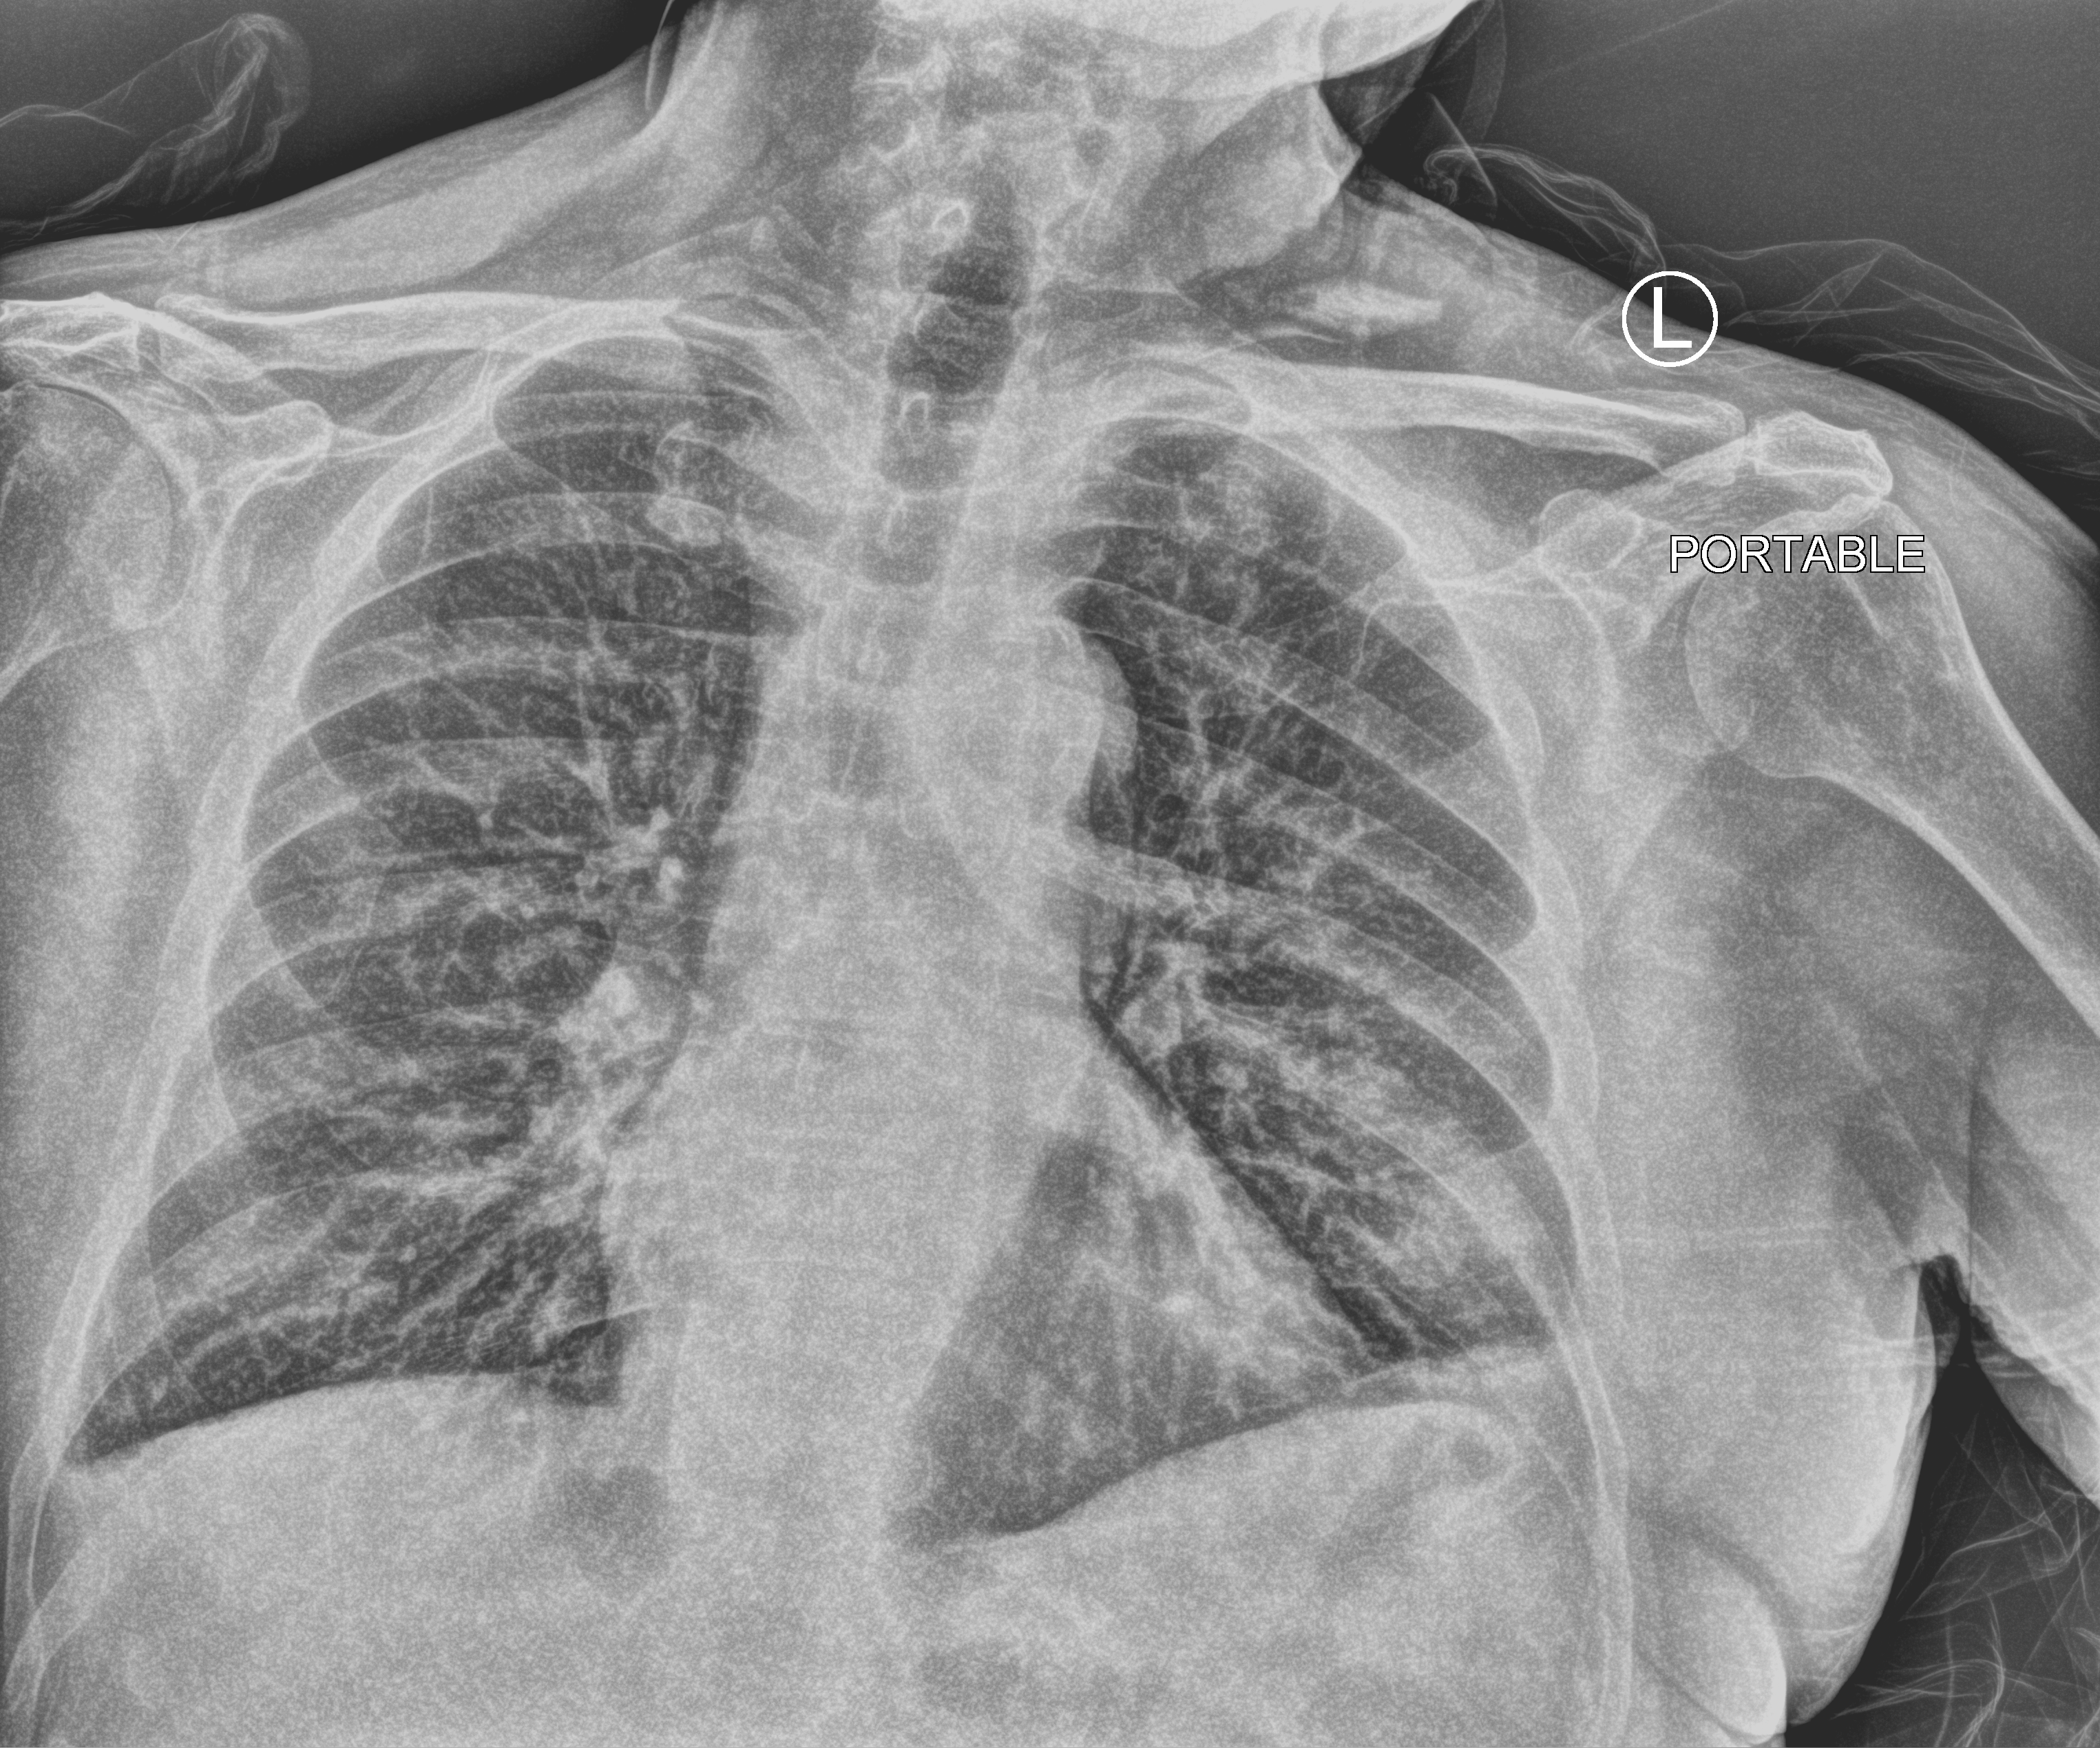
Chest X-ray (portable), anteroposterior (AP) projection. Patient hospitalised with COVID-19; male, aged 75–90 years.
Admission-level facts for this patient (not findings on this image; timing relative to this image not recorded):
- hypertension (admission record): no
- admitted to intensive care during this hospital stay: no
- mechanically ventilated during this hospital stay: no